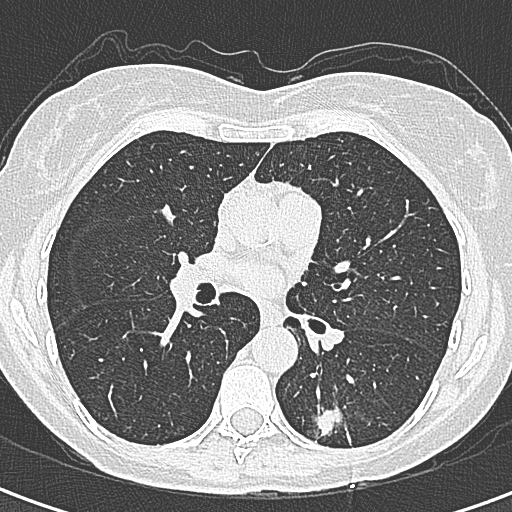
Chest CT (low-dose screening protocol), one axial image; first (baseline) screen; lung window (W 1500 / L -600 HU); slice 141 of 328 in the series; 512 × 512 image matrix, field of view 284 × 284 mm. Female participant, aged 58 years at enrolment.
- Expert-annotated lung lesion, bounding box [x1, y1, x2, y2] px = [299, 385, 368, 456].
- The screening reader recorded 2 non-calcified nodules or masses ≥4 mm on this exam; which of them this box marks is not recorded.
- Participant outcome: lung cancer diagnosed 22 days after this screen — adenocarcinoma, NOS, left lower lobe, moderately differentiated (G2), stage IA (AJCC 6th edition), 25 mm at pathology.